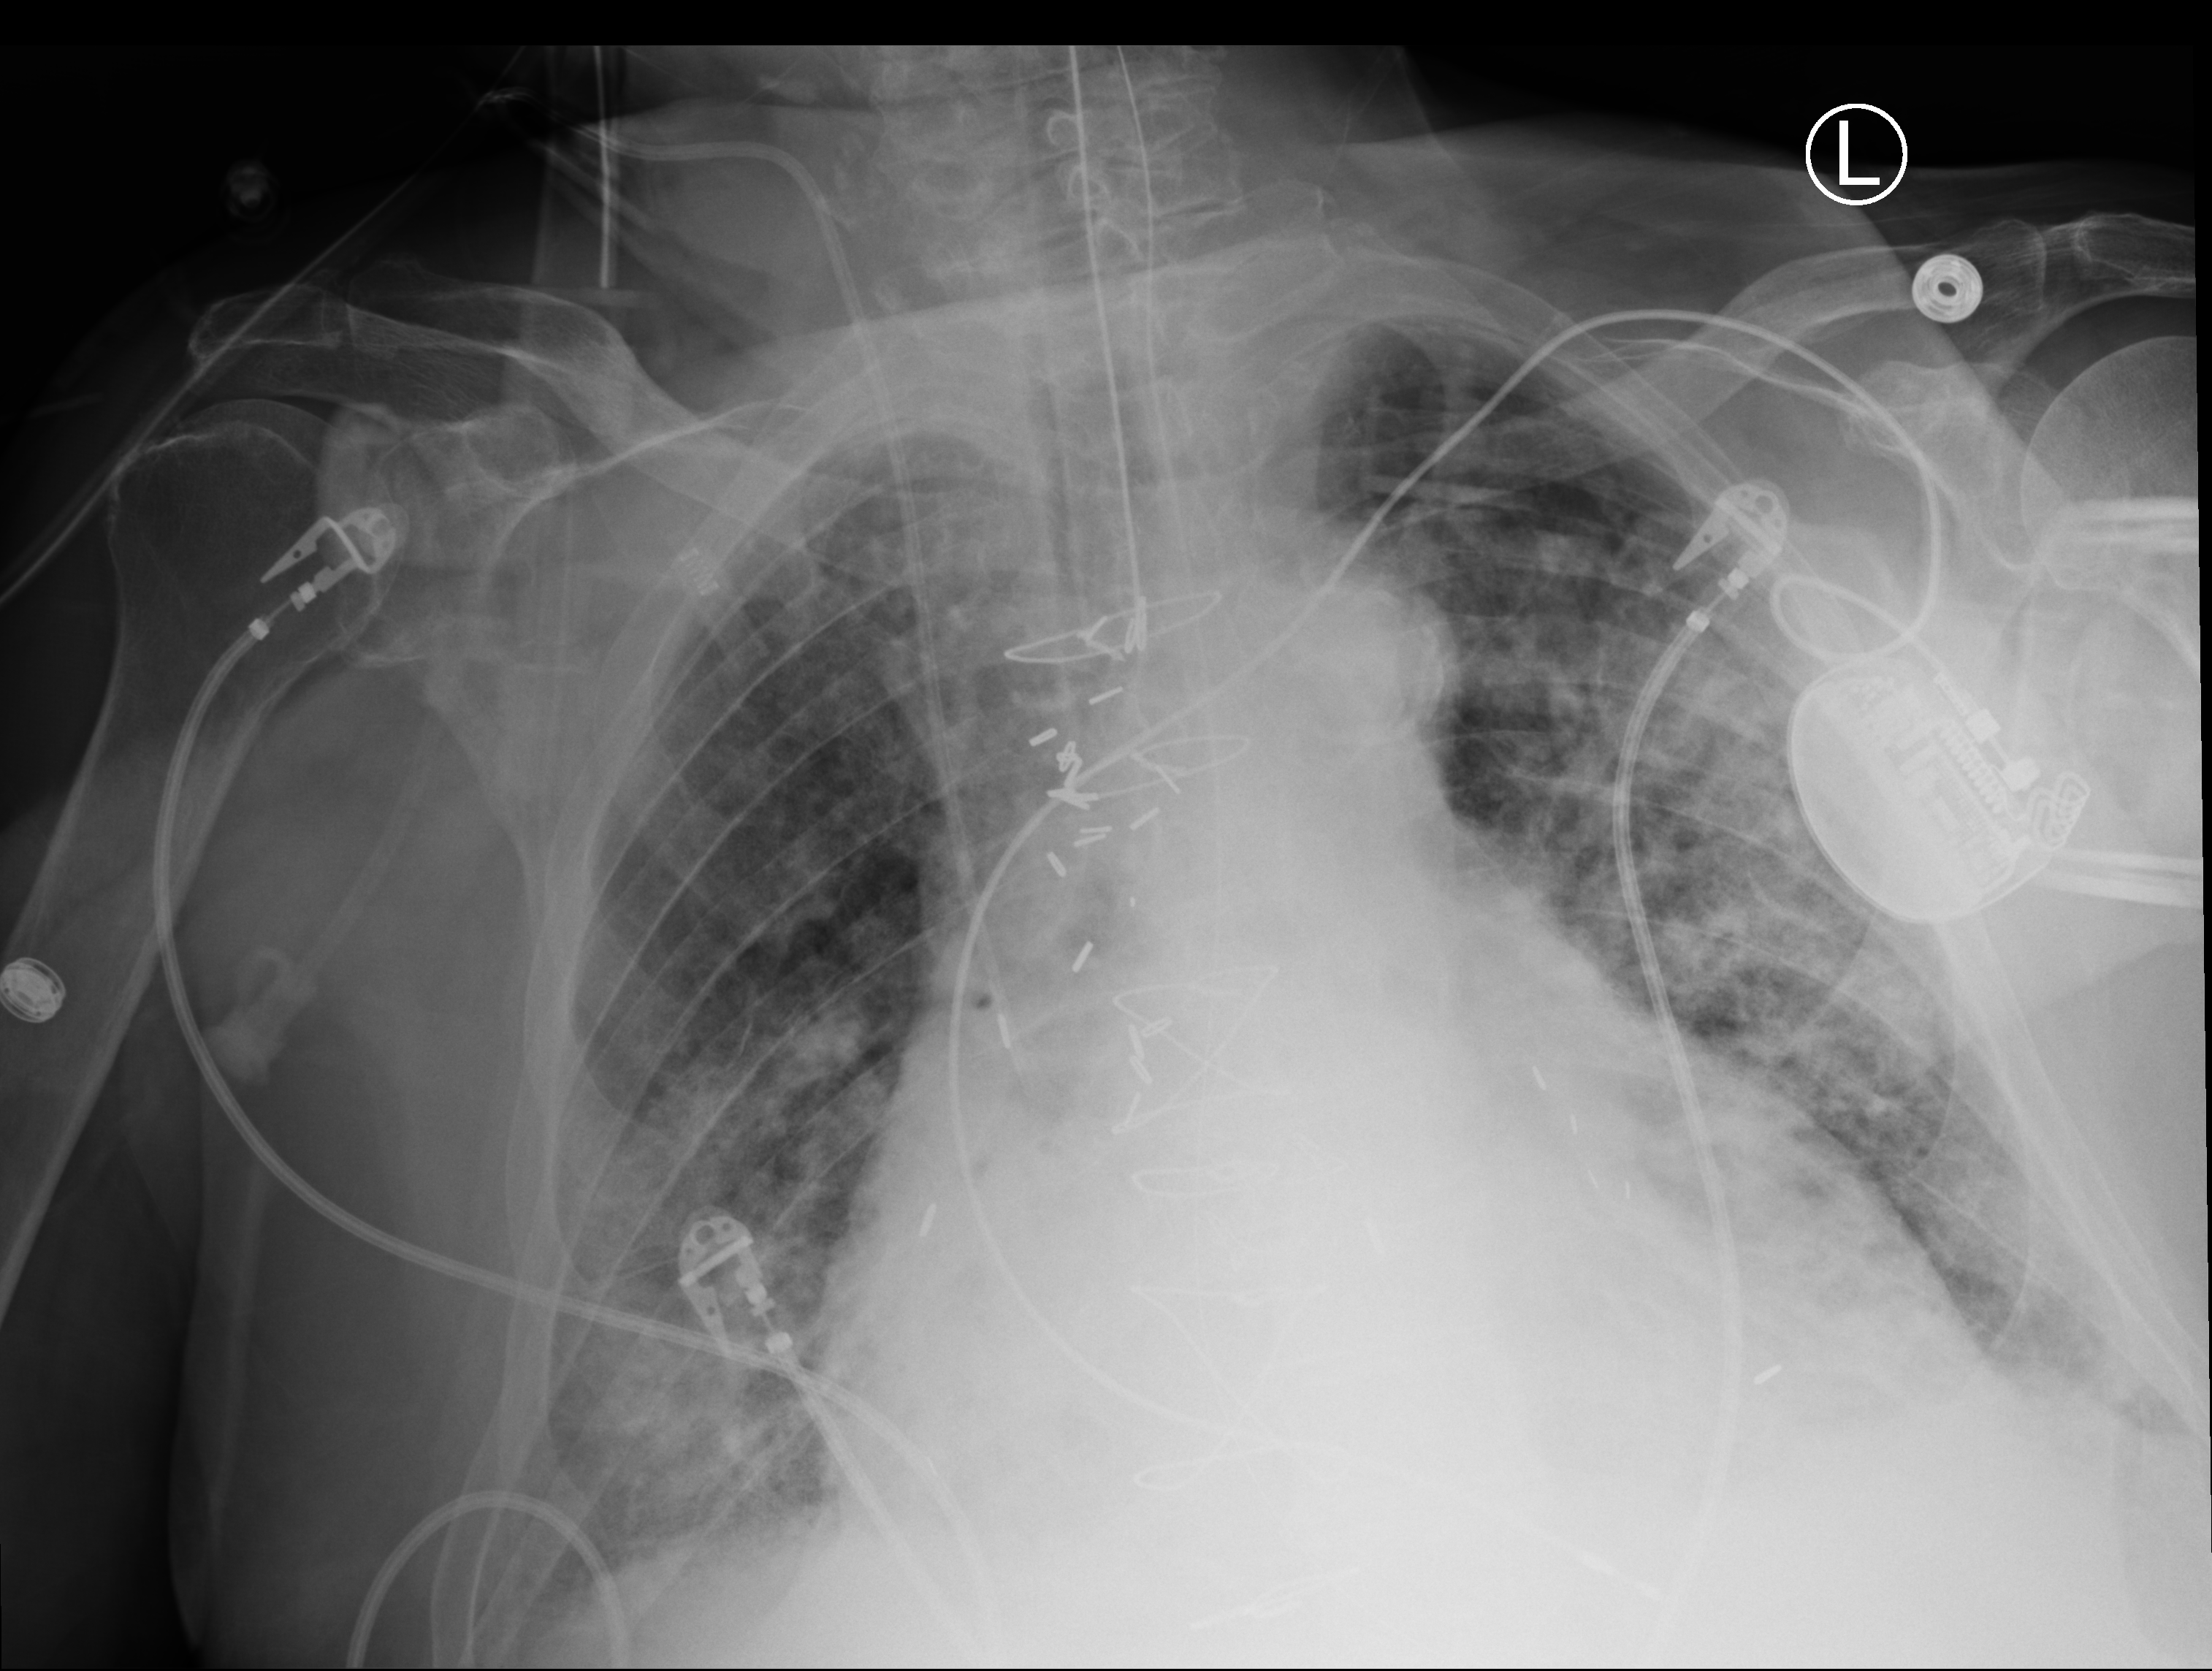
Chest X-ray (portable). Male patient hospitalised with COVID-19, age 75–90 years.
From the hospital-stay record, not from the radiograph (when in the stay this image was taken is not recorded): admitted to intensive care during this hospital stay: yes.